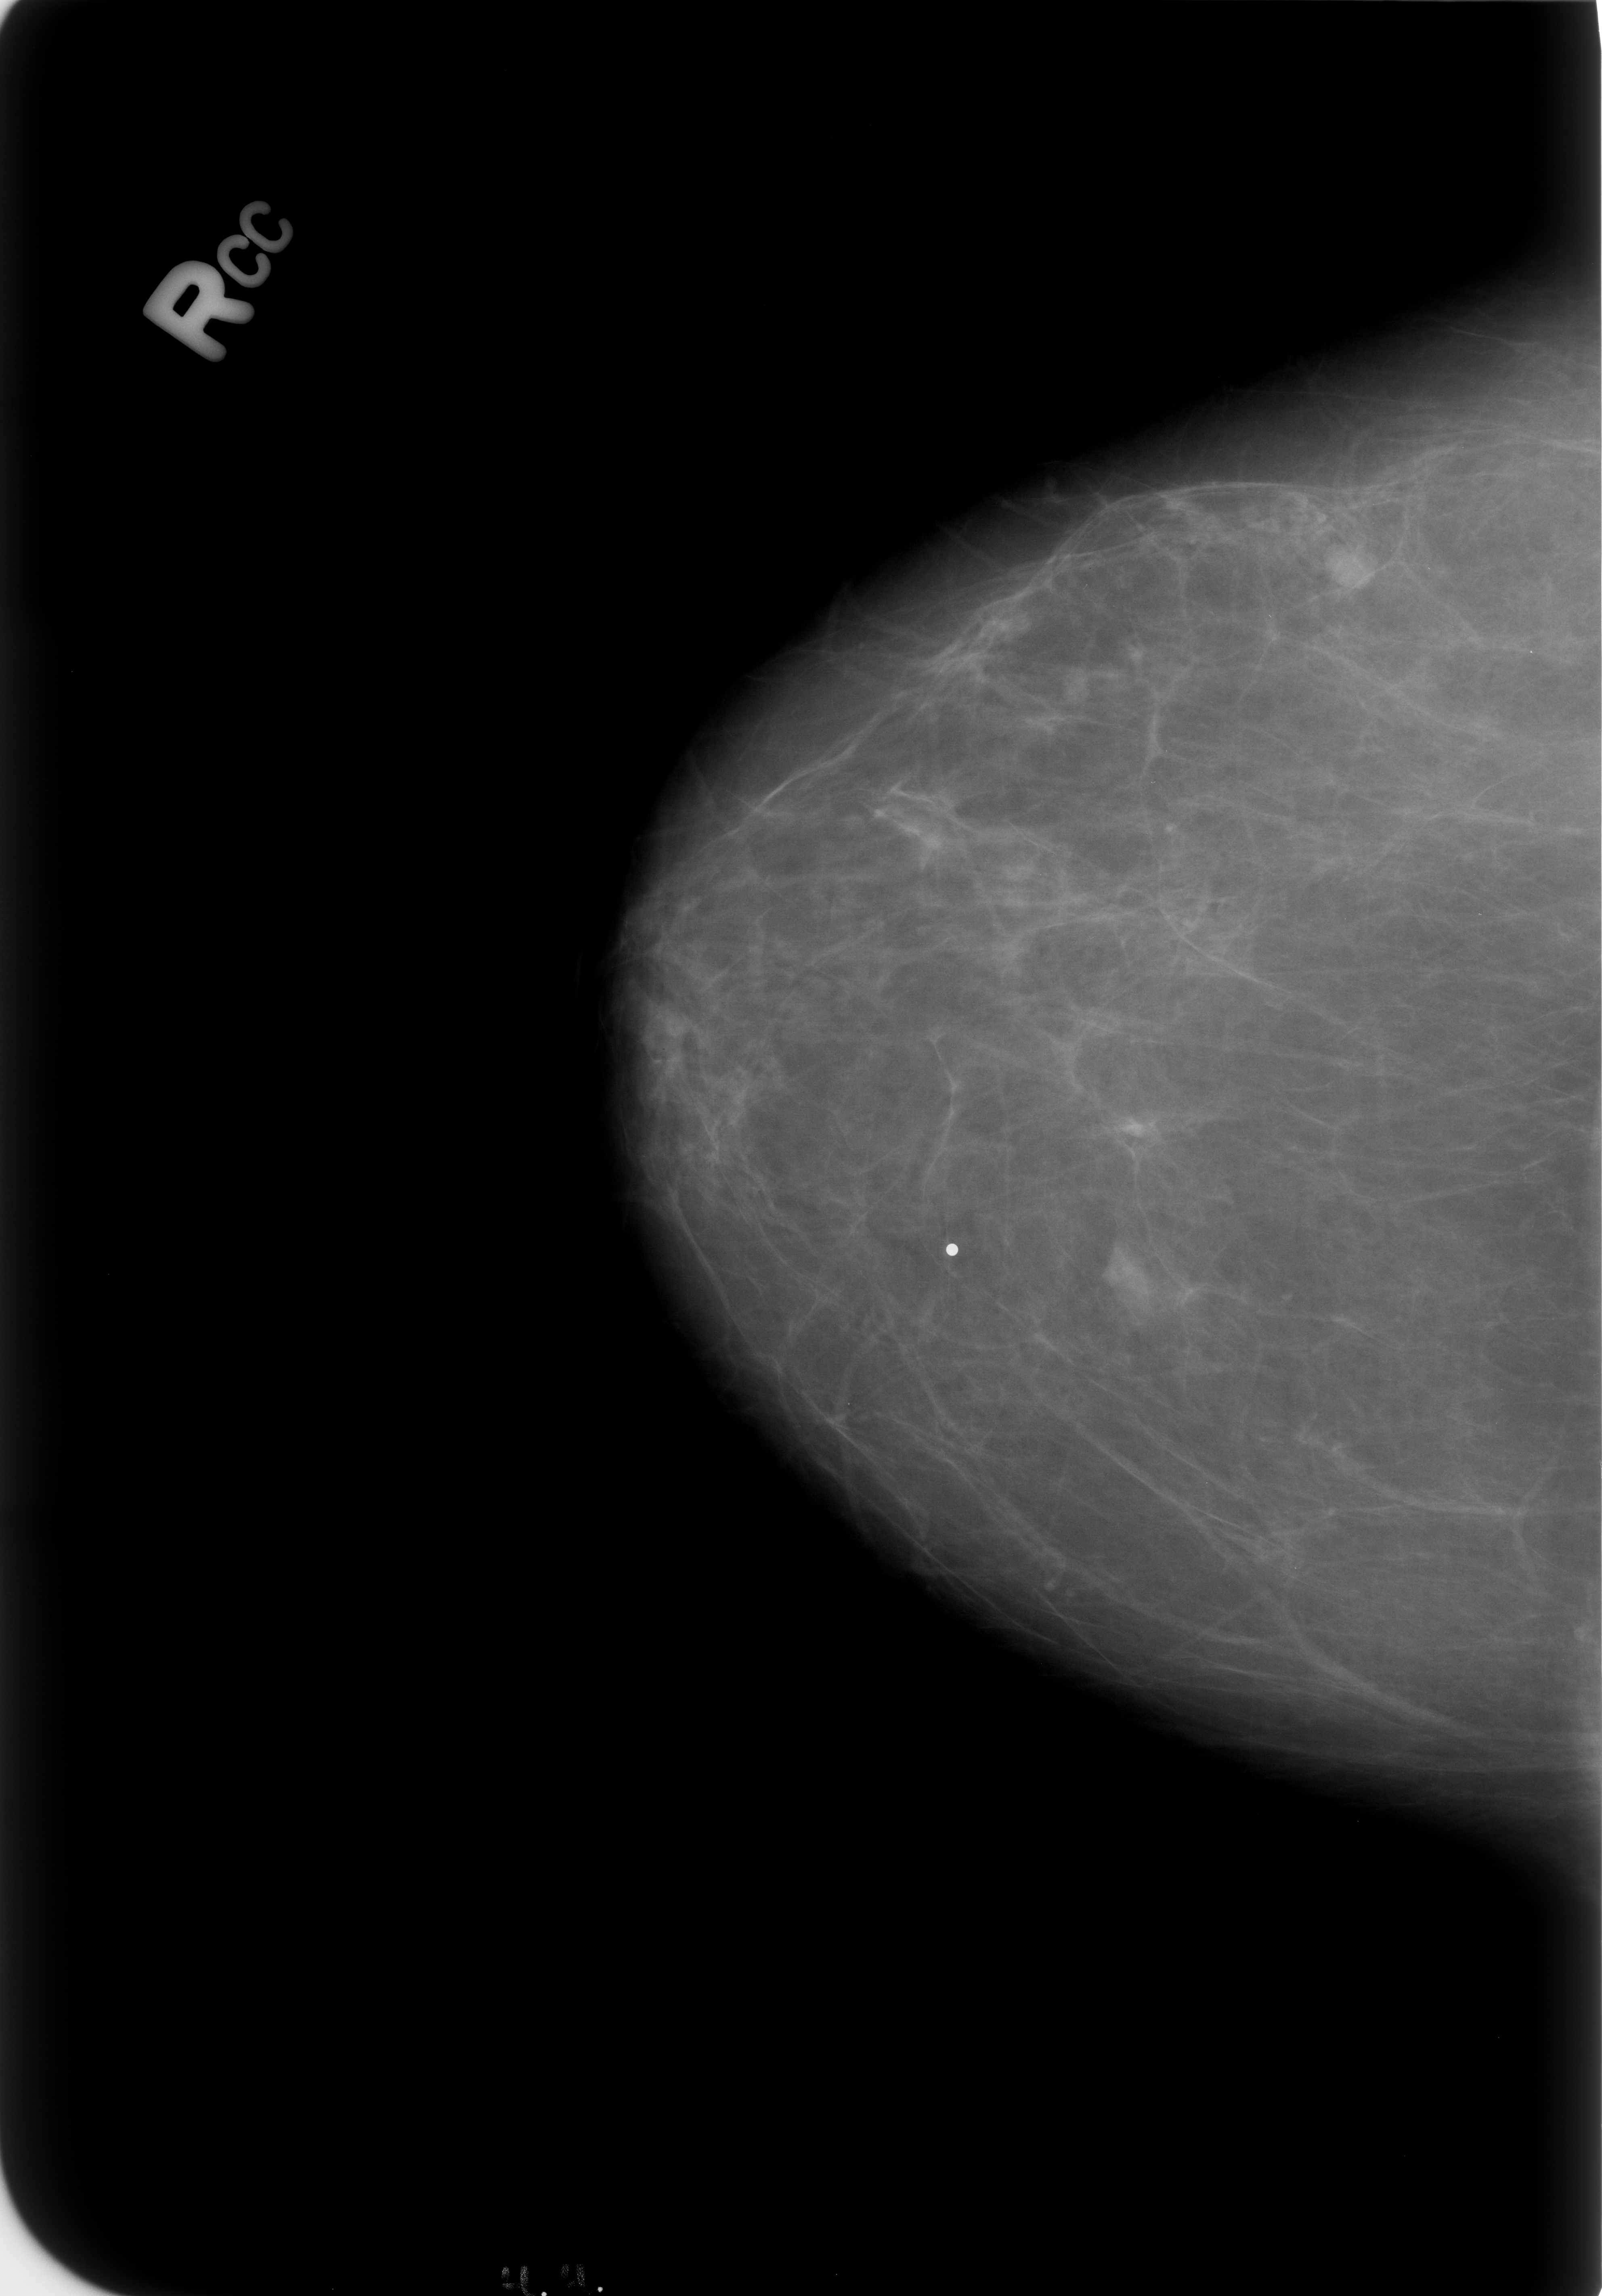
Mammogram (digitized film); right breast; CC view; BI-RADS breast density category 1 (scale 1–4); 1602 × 2296 image matrix.
Marked abnormalities (boxes around the expert regions of interest):
- mass, shape lymph node; BI-RADS assessment category 2; benign; no additional work-up was recommended (outcome (as recorded, no biopsy): benign without callback): box from (x=1312, y=531) to (x=1394, y=604) px